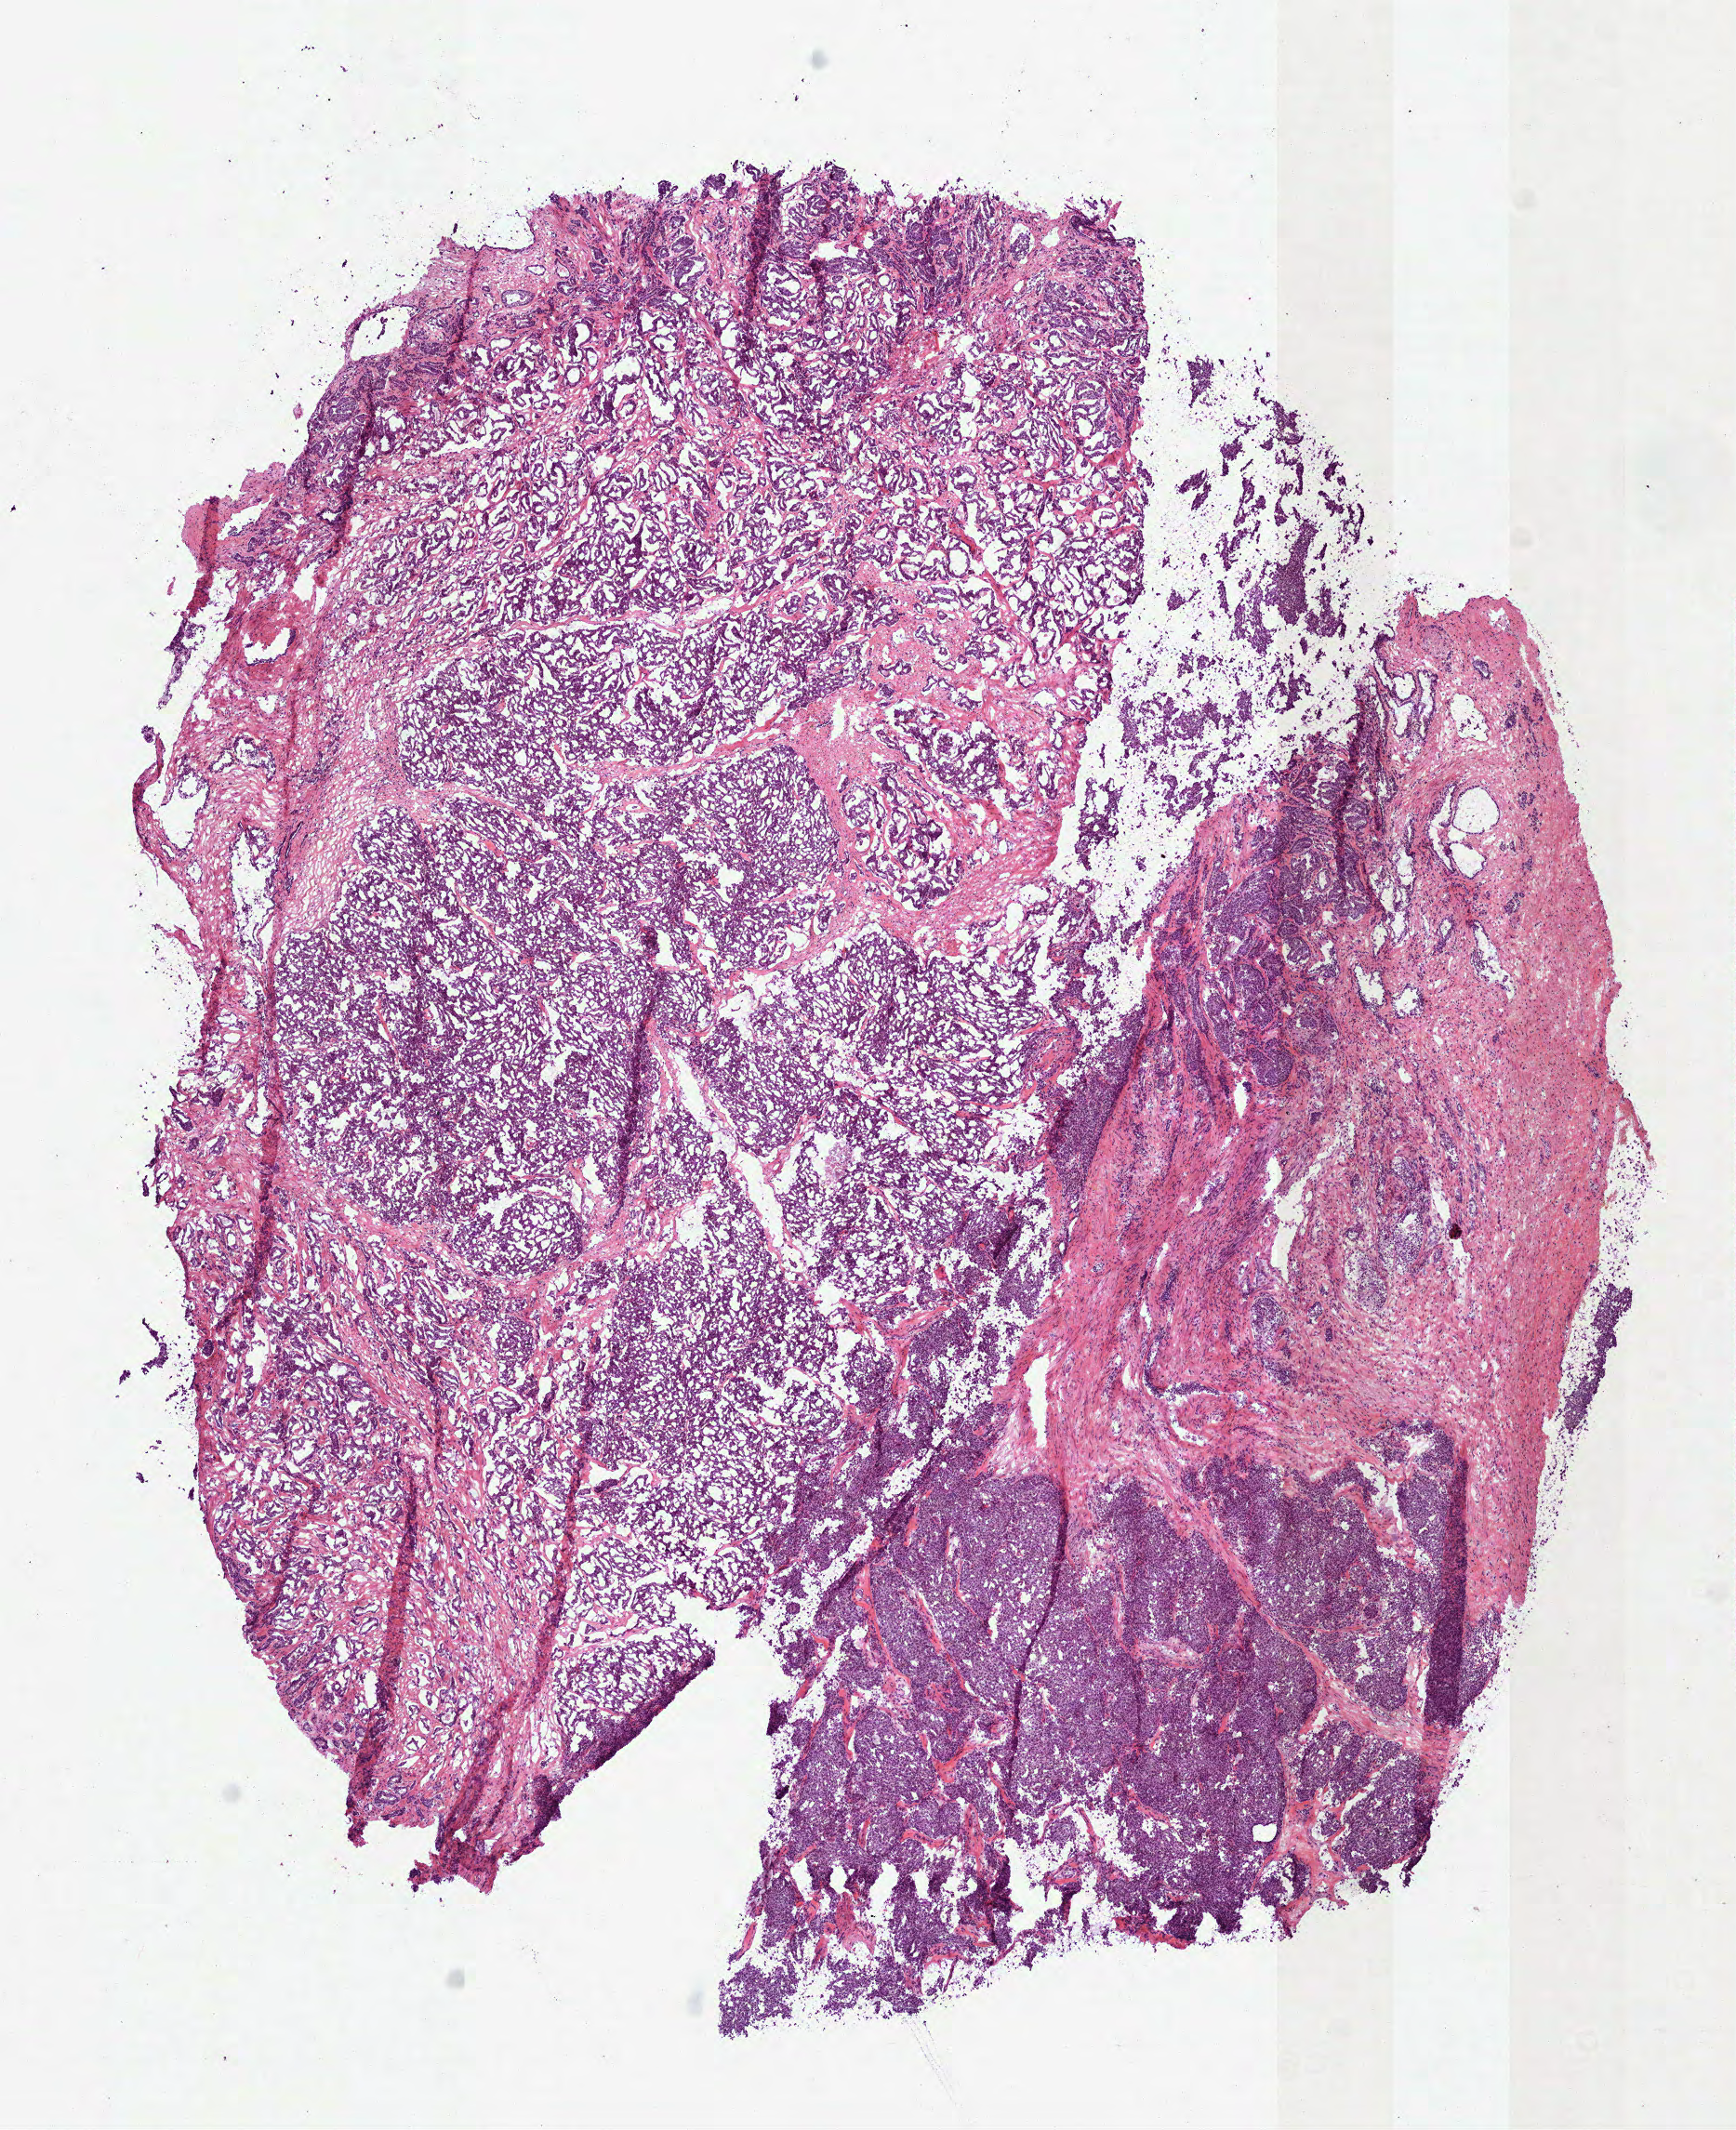
Whole-slide histology image, Hematoxylin and eosin (H&E) stained, low-resolution overview of the scanned area, about 7.5 x 9.2 mm (slide scanned at 40x), frozen section from the top of the tissue portion, primary tumour sample from the prostate. Patient: male, age at initial diagnosis 61 years. Gleason score: 7 (4+3). Slide review estimates, as recorded: tumour cells 80%, tumour nuclei 80%, normal cells 5%, stromal cells 15%, necrosis 0%. Infiltration values recorded for this section: lymphocyte infiltration 2%, monocyte infiltration 0%, neutrophil infiltration 0%.
* pathologic diagnosis: Acinar cell carcinoma (prostate gland)